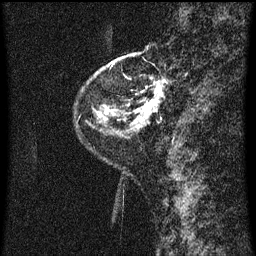
Breast MRI (dynamic contrast-enhanced), one sagittal slice; position 9 of 60 along the scan axis; dynamic contrast-enhanced series, image 2 of 3 at this slice position (ordered by acquisition); 1.5 T; TE 4.2 ms, TR 8 ms; 2 mm slice thickness; 256 × 256 image matrix, field of view 180 × 180 mm. Patient: female, 48 years.
Outlined on this slice (semi-automatically segmented with operator editing):
- analysis volume of interest (the breast-tissue region the enhancement analysis was run in; not a lesion): bounding box <128,54,174,125> (left, top, right, bottom; pixels)
- tumour enhancement mask (voxels above the 70 % enhancement threshold inside the analysis volume of interest): <135,78,167,121>